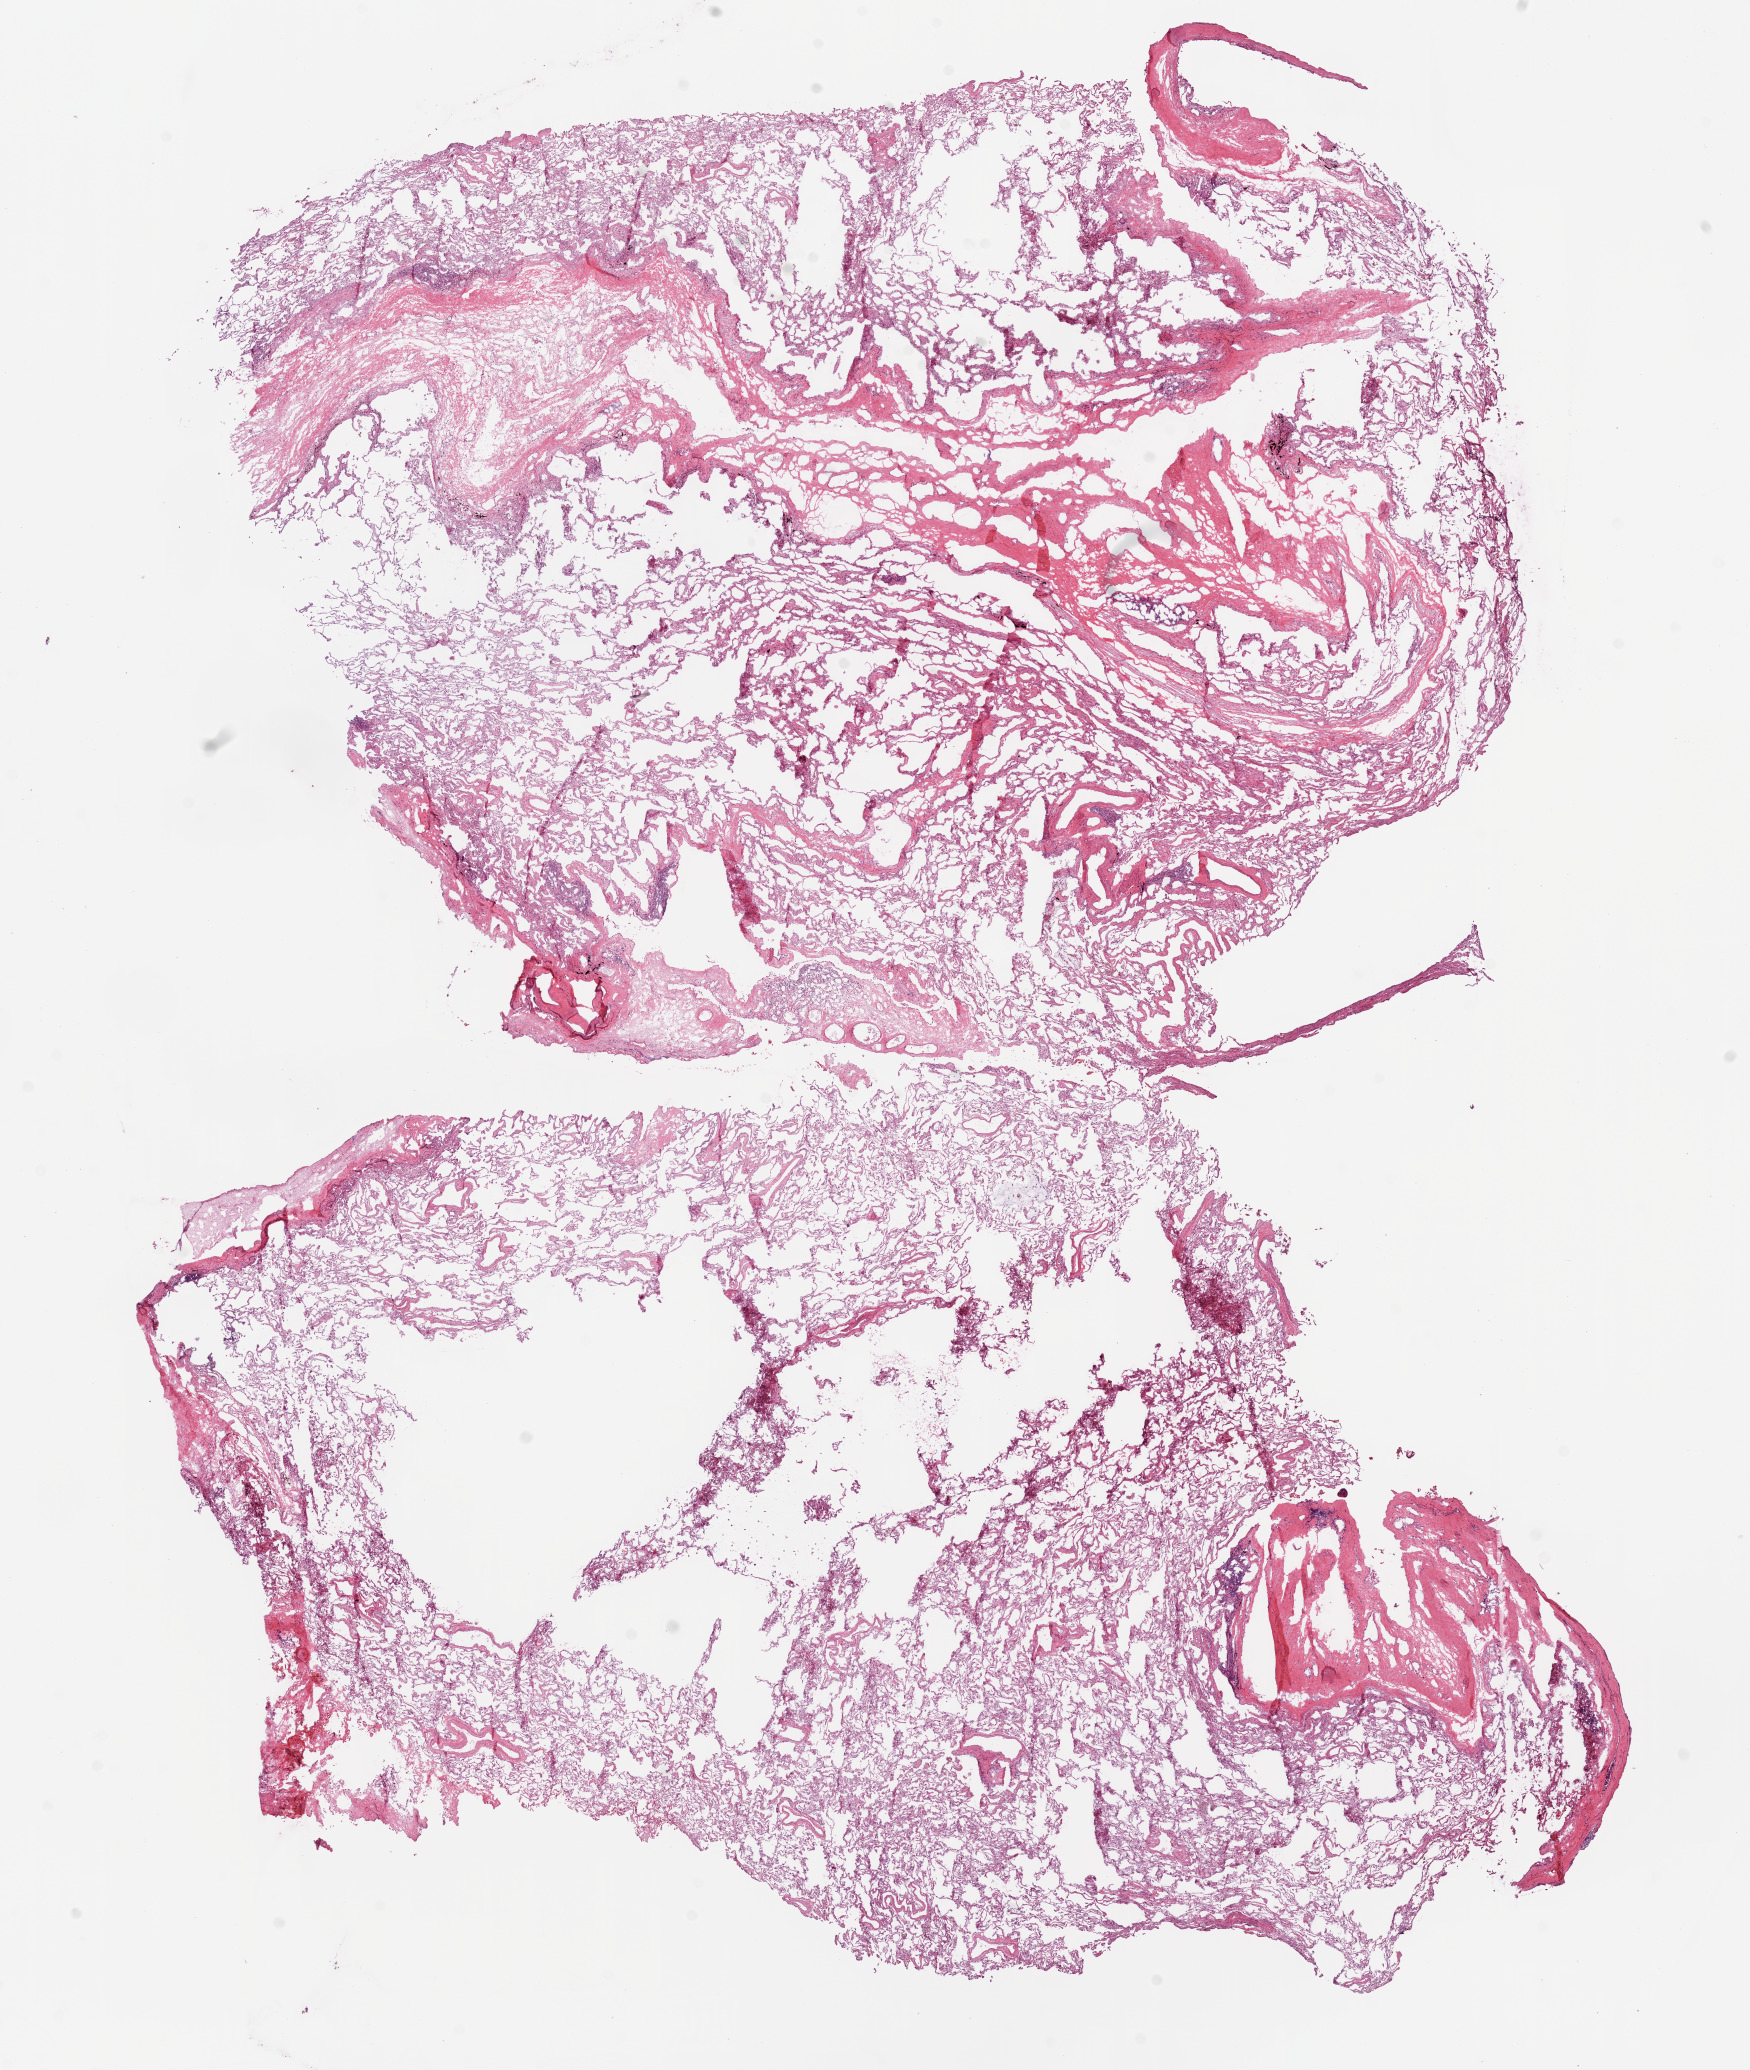
Digitized H&E-stained tissue section (whole slide) — a low-resolution overview of the entire scanned area, about 14.0 x 16.6 mm; frozen section from the top of the tissue portion; solid tissue normal (non-tumour tissue) sample from the lung. Male, age 65 years at initial diagnosis.
This section: solid tissue normal (non-tumour) sample from the same patient. Patient diagnosis: Squamous cell carcinoma, NOS (lower lobe, lung).